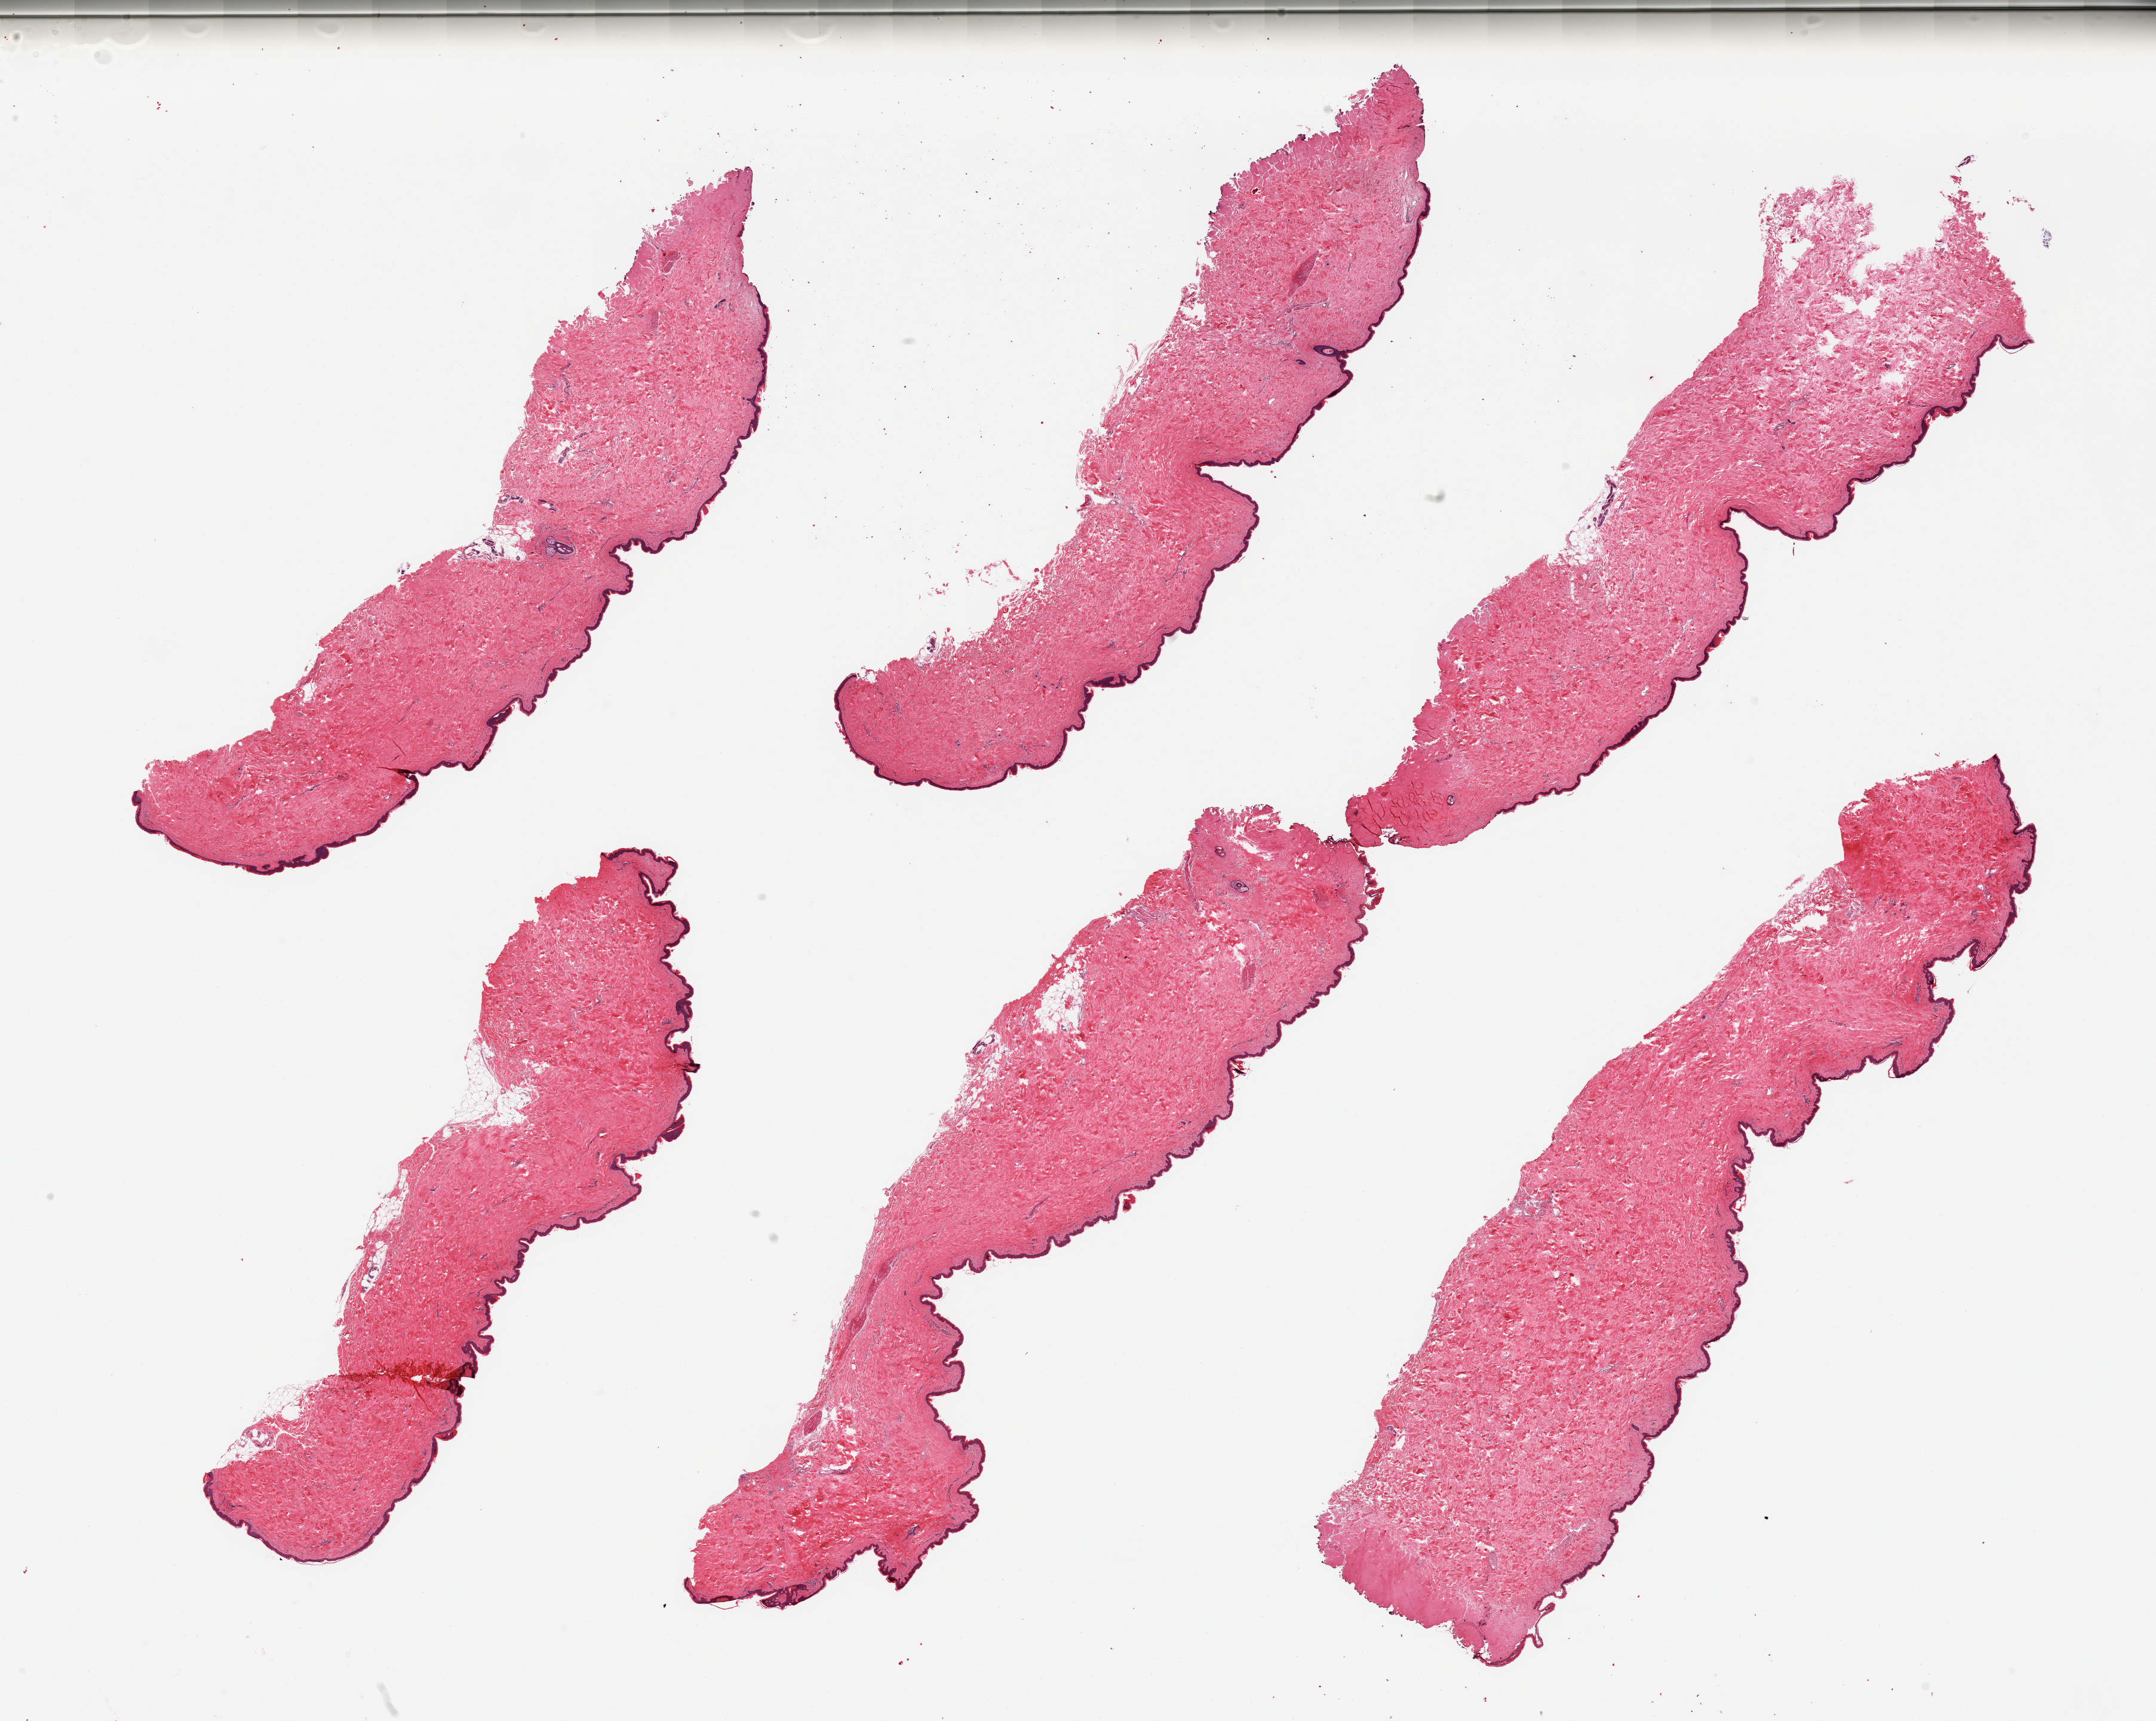
Whole-slide image, haematoxylin and eosin stain, shown as a low-resolution overview of the whole scanned area (about 28.5 x 22.8 mm). PAXgene-fixed paraffin-embedded (PFPE) section. Section of skin of suprapubic region (target tissue). Donor tissue sample. Donor sex: female.
- review note (as recorded): 6 pieces, minimal dermal fat; squamous epithelium is ~50 microns